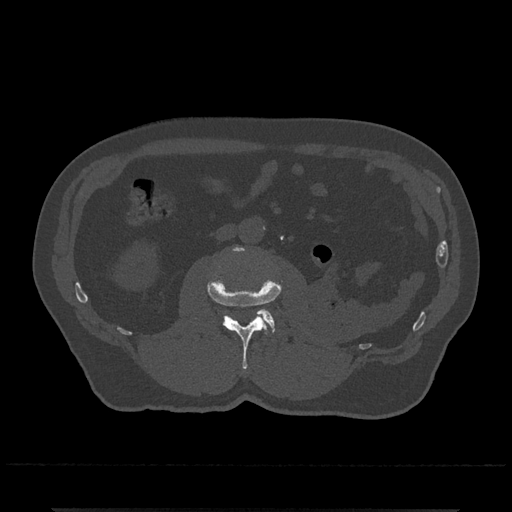
CT including the spine, one axial slice. Slice 275 of 797 in the series (ordered by position). Bone window (W 1800 / L 400 HU). 0.5 mm slice thickness. 512 × 512 image matrix, field of view 393 × 393 mm. Male patient, age 67 years. Case-level facts recorded for this patient, not image findings: primary cancer: prostate.
Structures marked on this image (semi-automatically segmented with operator editing):
- L2 vertebra: bounding box [x1, y1, x2, y2] px = [207, 247, 281, 369]
- L3 vertebra: [223, 309, 275, 331]